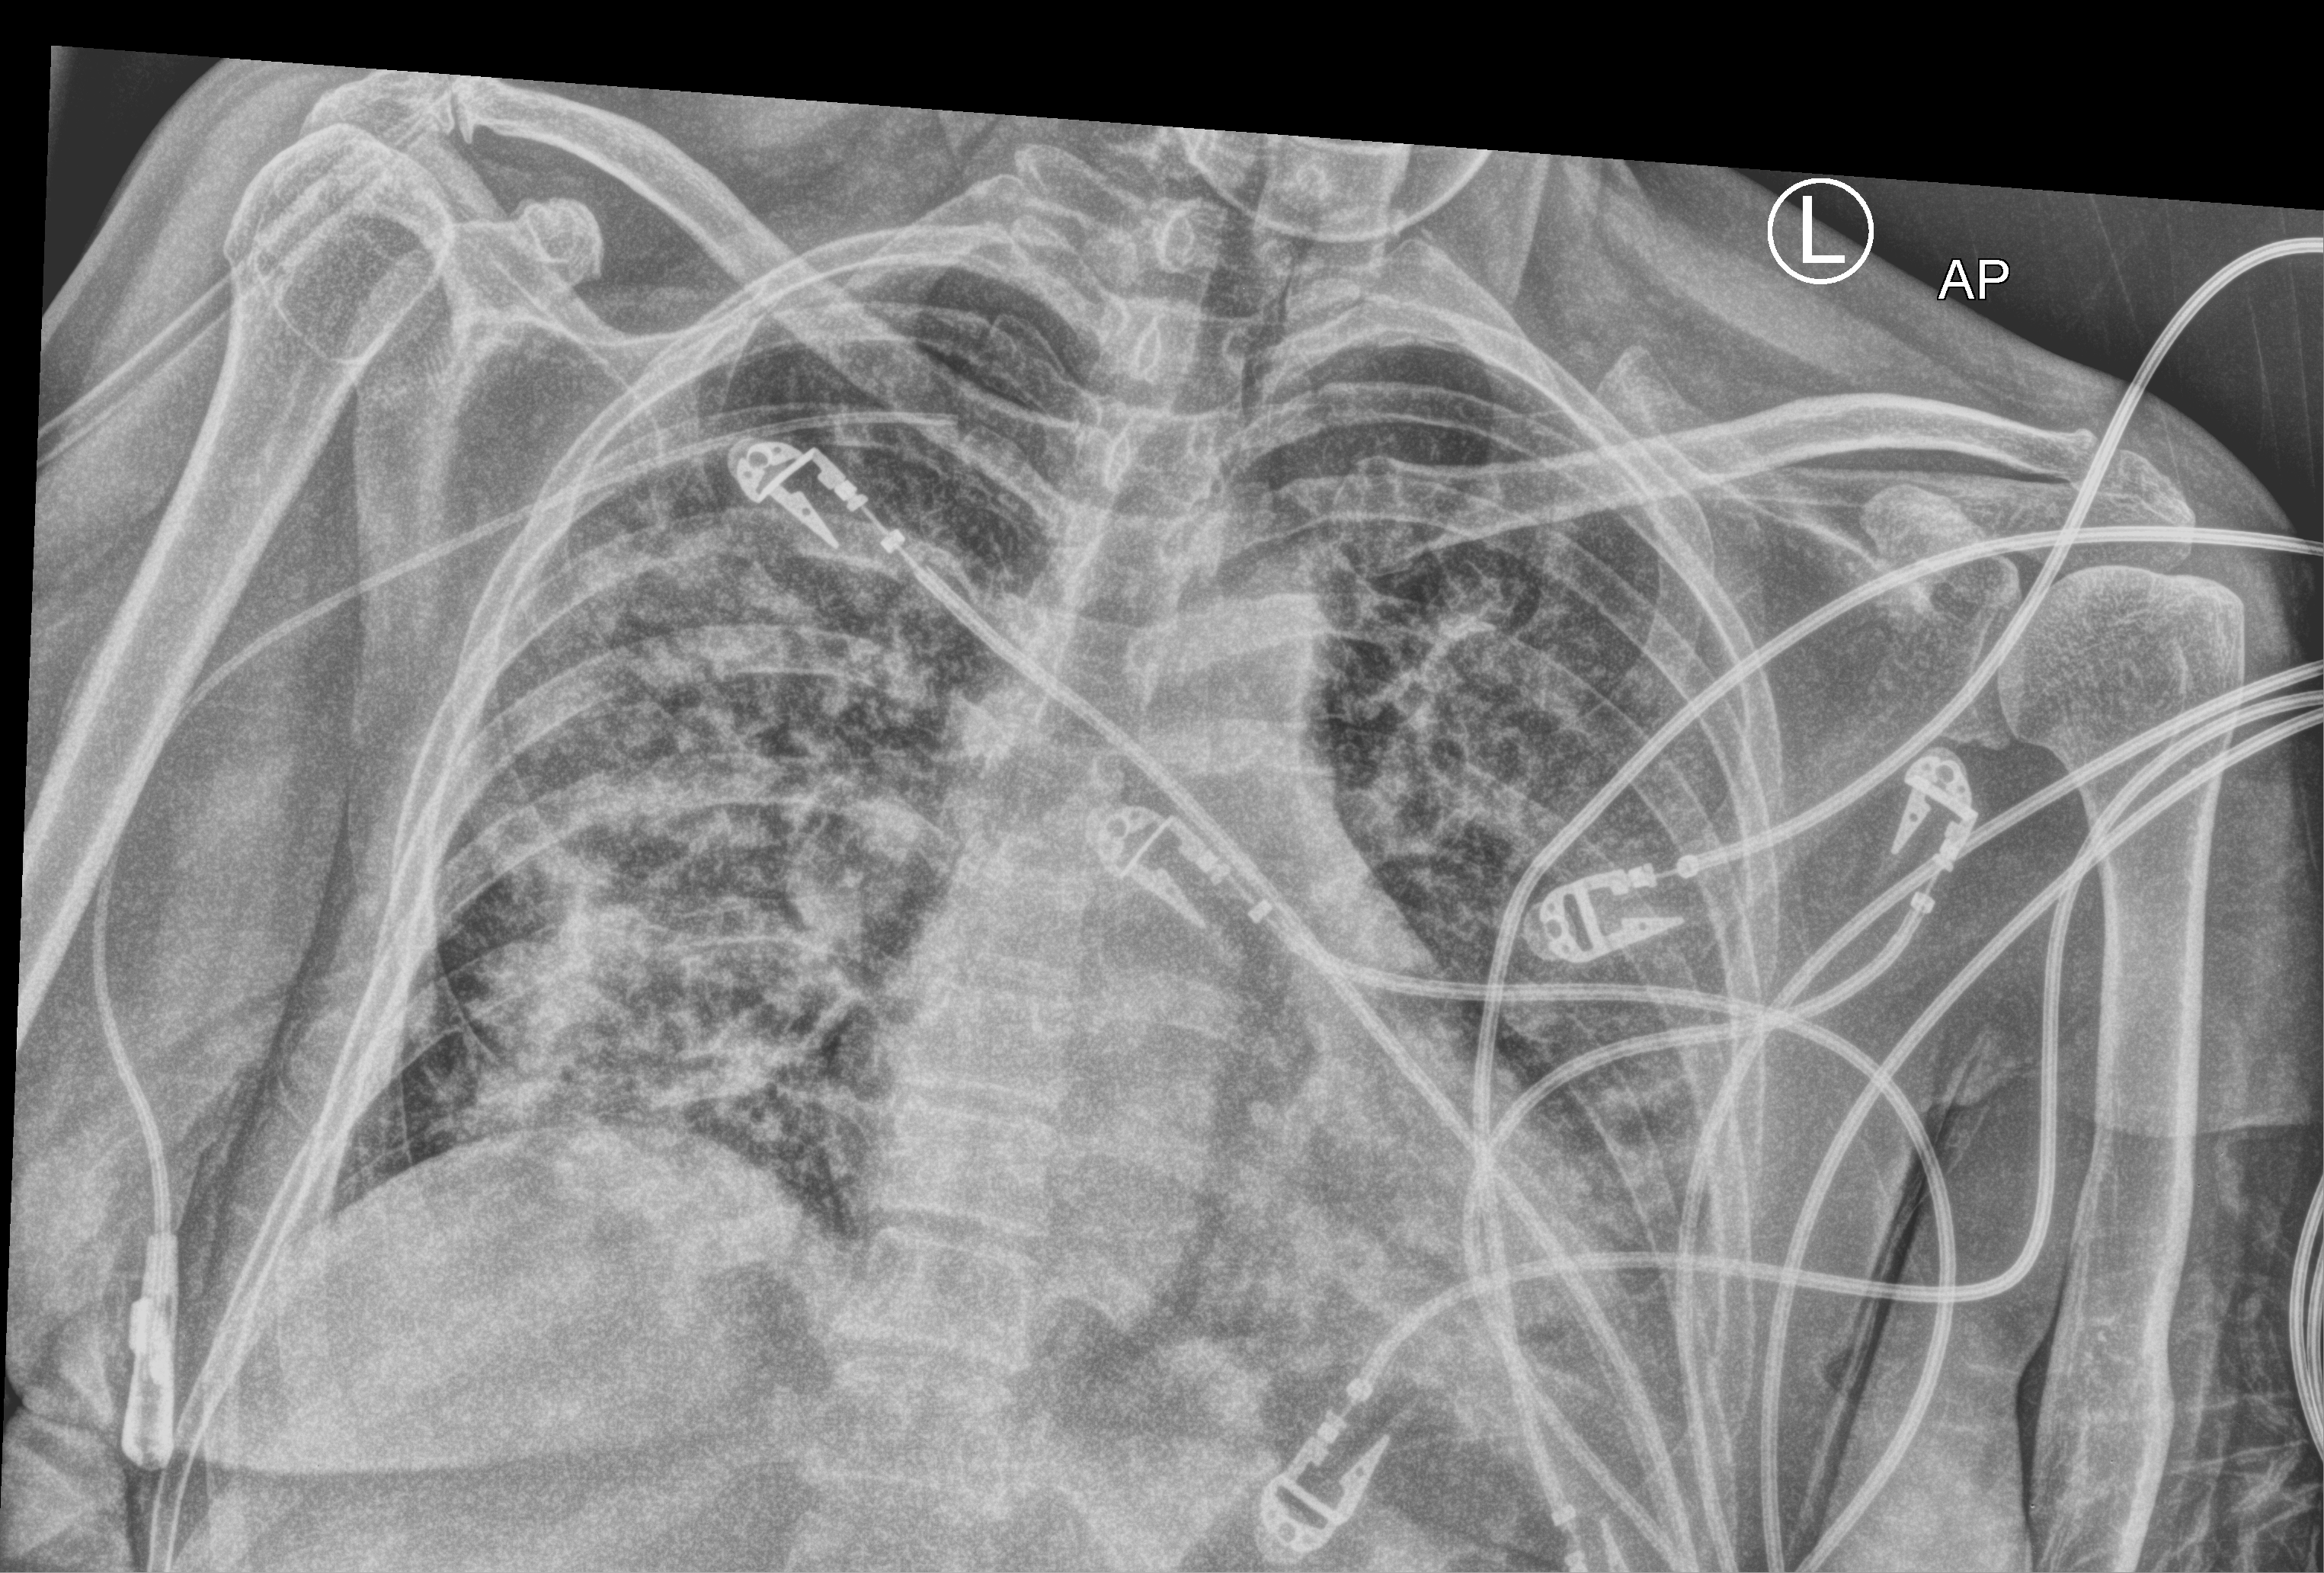
Portable chest radiograph; anteroposterior (AP) projection. Patient hospitalised with COVID-19; female, aged 60–74 years.
Admission-level facts for this patient (not findings on this image; timing relative to this image not recorded):
- length of hospital stay: 14 days